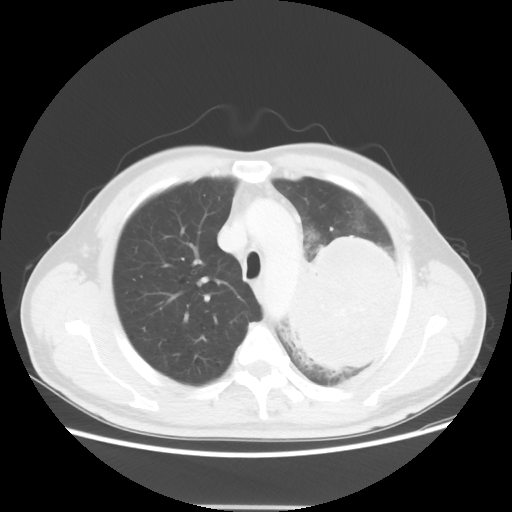
Chest CT, one axial slice; position 41 of 53 along the scan axis; reconstruction kernel STANDARD; lung window (W 1500 / L -600 HU); 512 × 512 image matrix, field of view 391 × 391 mm. Patient: male, 60 years. From the clinical record (not read from this slice): clinical TNM (as recorded): T4 N1 M1a; histopathological grade: G3.
Structures marked on this image (rectangle marked by the reading radiologist):
- lung tumour (recorded histology: large cell carcinoma): box from (x=279, y=234) to (x=413, y=379) px